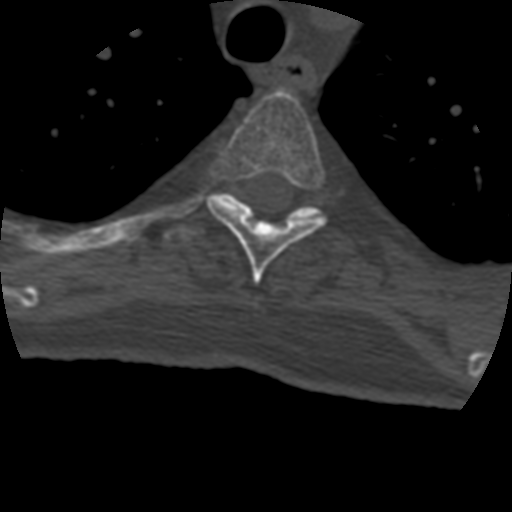
CT including the spine, one axial slice; slice 333 of 399 in the series (ordered by position); reconstruction kernel STANDARD; bone window (W 1800 / L 400 HU); 512 × 512 image matrix. Patient age 69 years. From the clinical record (not read from this slice): primary cancer: prostate.
Annotated regions visible in this slice (semi-automatically segmented with operator editing):
- T4 vertebra: bounding box [x1, y1, x2, y2] px = [208, 90, 327, 285]
- T5 vertebra: [162, 193, 321, 250]